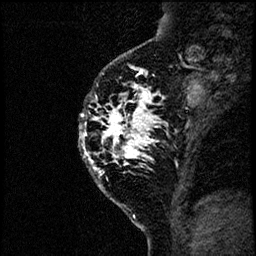
Breast MRI (dynamic contrast-enhanced), one sagittal slice. Position 47 of 60 along the scan axis. Dynamic contrast-enhanced study with each time point stored as its own series, time point 2 of 4 at this slice position (early post-contrast, ordered by acquisition time). 1.5 T. TE 4.2 ms, TR 17.6 ms. 2 mm slice thickness. 256 × 256 image matrix. Patient: female, 40 years. From the clinical record (not read from this slice): setting: breast cancer imaged before/during neoadjuvant chemotherapy; receptor status: HER2-positive.
Outlined on this slice (semi-automatic segmentation, software-assisted and operator-edited):
- analysis volume of interest (the breast-tissue region the enhancement analysis was run in; not a lesion): box from (x=74, y=55) to (x=185, y=206) px
- tumour enhancement mask (voxels above the 100 % enhancement threshold inside the analysis volume of interest): (x=79, y=72)–(x=162, y=162)